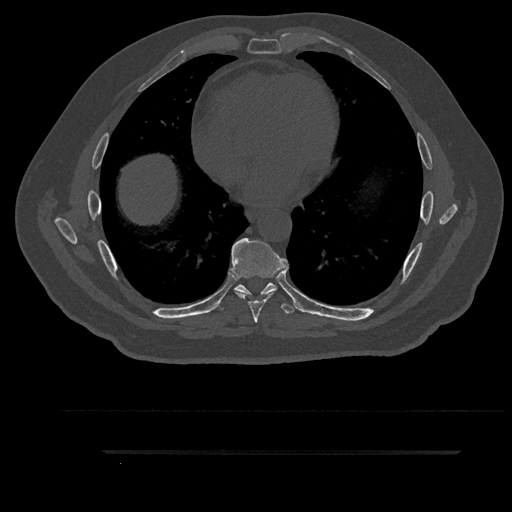
CT including the spine, one axial slice. Position 506 of 797 along the scan axis. Reconstruction kernel Br40s/3. 120 kVp. Bone window (W 1800 / L 400 HU). 0.5 mm slice thickness. 512 × 512 image matrix, field of view 432 × 432 mm. Male patient, age 63 years. From the clinical record (not read from this slice): primary cancer: renal; vertebrae with lytic lesions (as recorded): T8.
Annotated regions visible in this slice (semi-automatically segmented with operator editing):
- T6 vertebra: box from (x=242, y=293) to (x=269, y=296) px
- T7 vertebra: (x=230, y=238)–(x=289, y=323)
- T8 vertebra: (x=215, y=283)–(x=299, y=314)